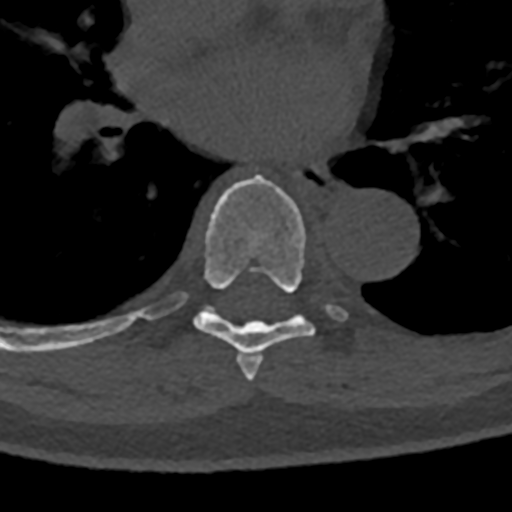
CT including the spine, one axial slice. Slice 759 of 797 in the series (ordered by position). Reconstruction kernel Br40s/3. 120 kVp. Bone window (W 1800 / L 400 HU). 0.5 mm slice thickness. 512 × 512 image matrix, field of view 160 × 160 mm. Patient: male, 74 years. From the clinical record (not read from this slice): primary cancer: renal; vertebrae with lytic lesions (as recorded): T10, L1, L2, L3, L4, L5.
Annotated regions visible in this slice (semi-automatic segmentation, software-assisted and operator-edited):
- T6 vertebra: bounding box (x1, y1, x2, y2) in pixels: (245, 356, 263, 381)
- T7 vertebra: (70, 175, 347, 373)
- T8 vertebra: (70, 314, 140, 347)